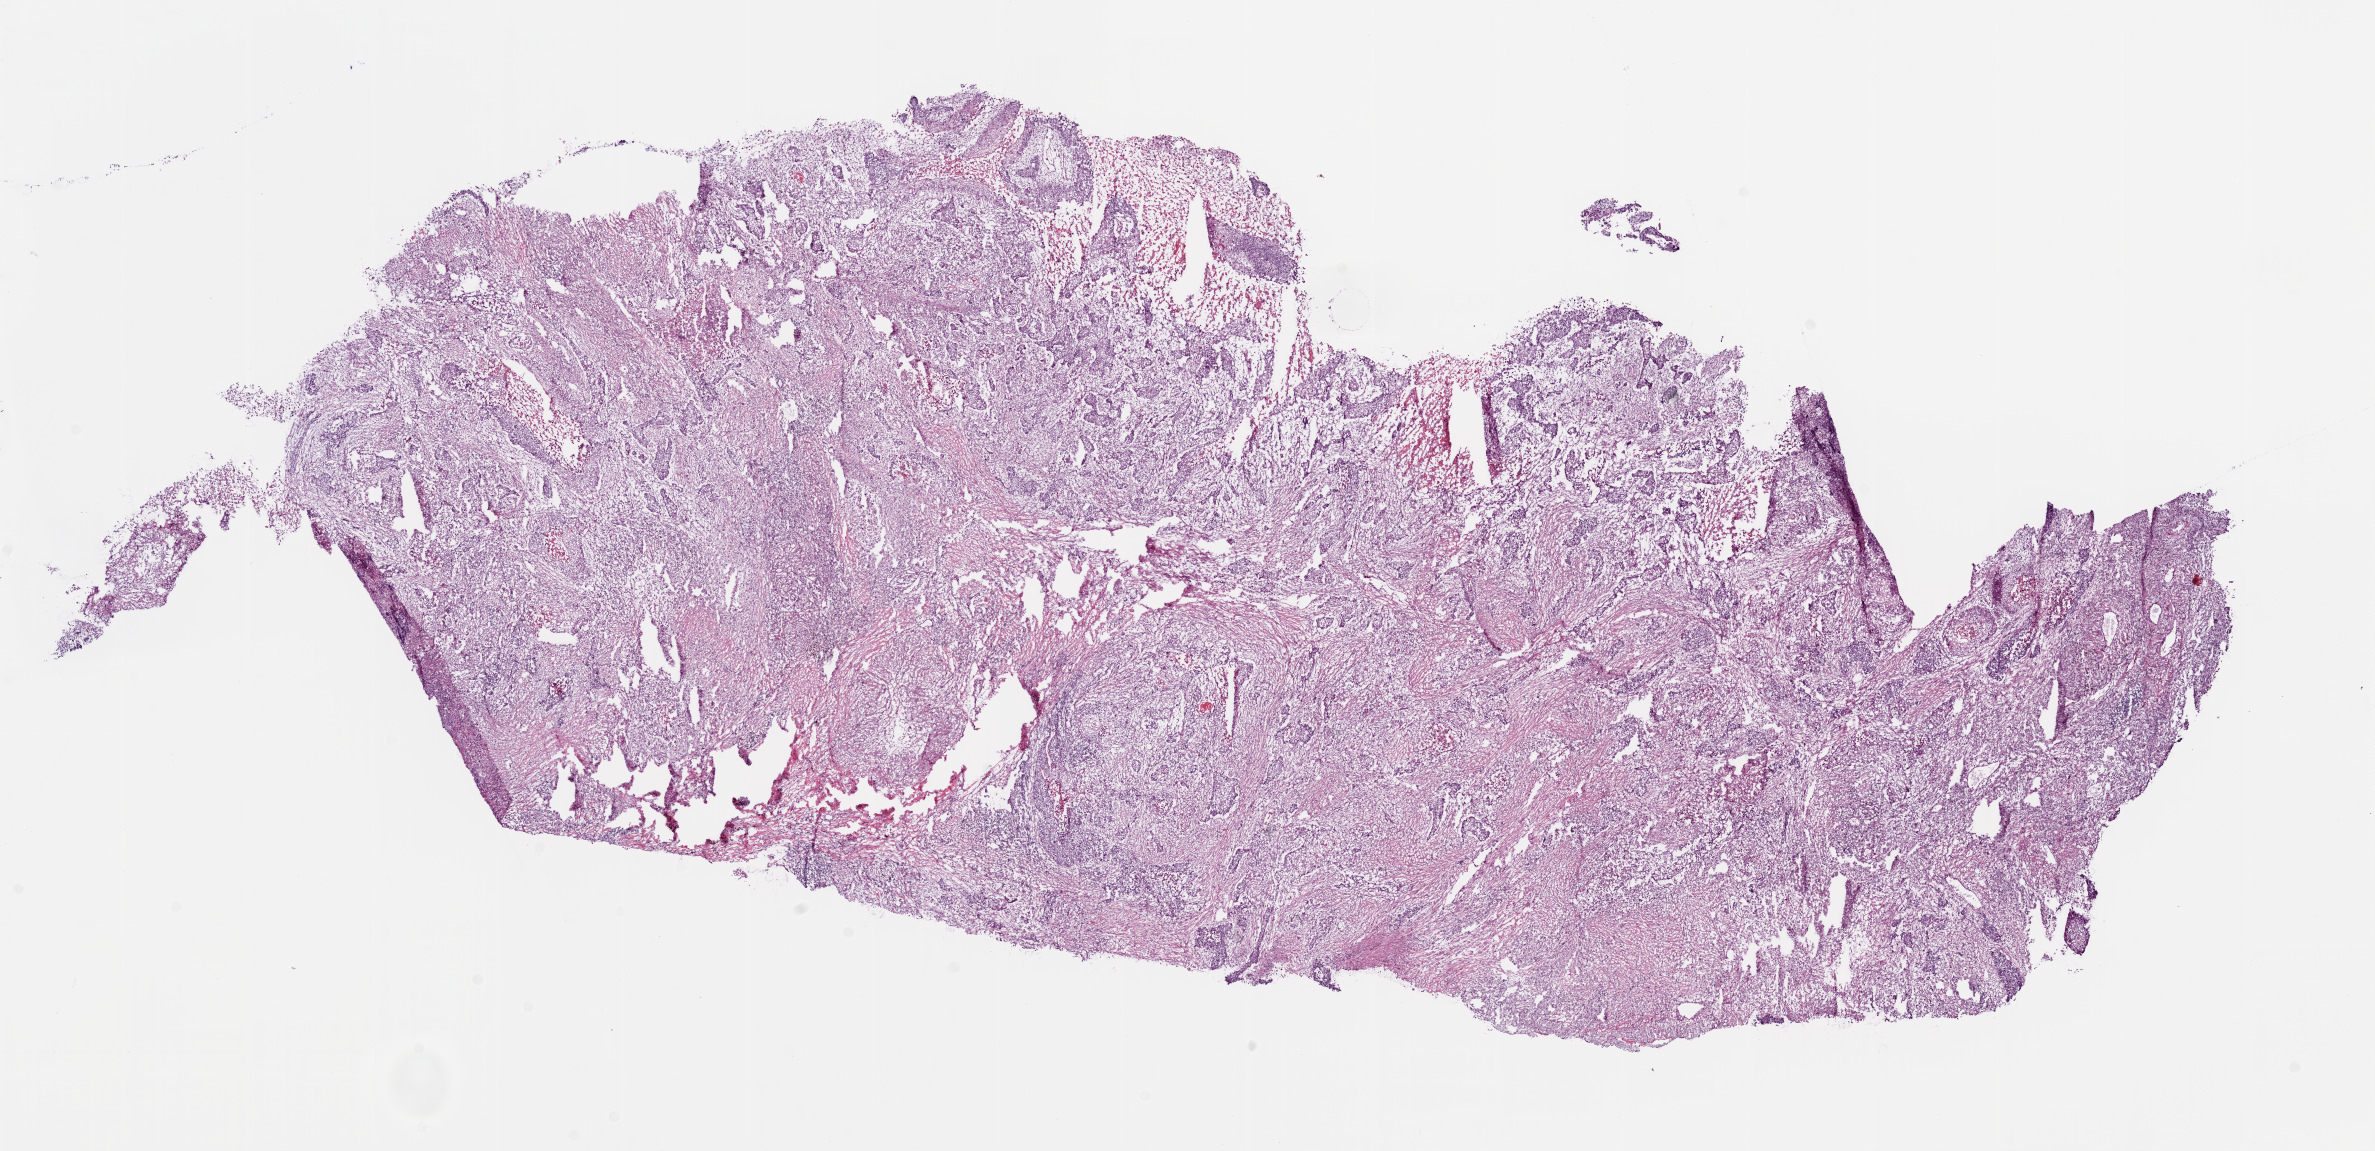
Whole-slide histology image, H&E — a low-resolution overview of the entire scanned area, about 19.1 x 9.2 mm (slide scanned at 20x); frozen section from the bottom of the tissue portion; lung, primary tumour sample. Male patient; age at initial diagnosis 60 years. Composition of this section per pathologist review: tumour cells 60%, tumour nuclei 70%.
Histologic diagnosis: Squamous cell carcinoma, NOS (upper lobe, lung).